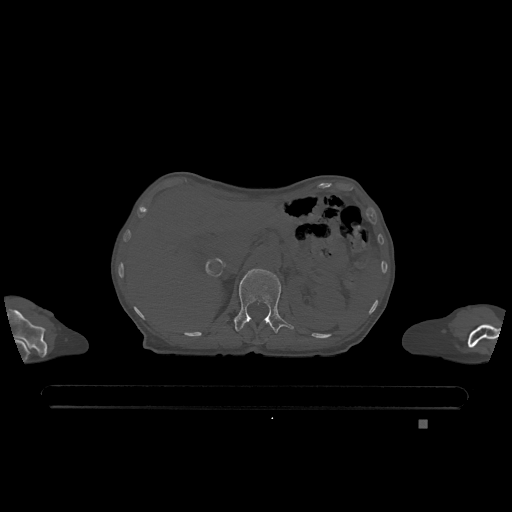
CT including the spine, one axial slice. Position 484 of 1317 along the scan axis. Bone window (W 1800 / L 400 HU). 0.5 mm slice thickness. 512 × 512 image matrix. Patient: female, 74 years. Case-level facts recorded for this patient, not image findings: primary cancer: lung.
Annotated regions visible in this slice (semi-automatically segmented with operator editing):
- L1 vertebra: bounding box <234,269,294,333> (left, top, right, bottom; pixels)
- T12 vertebra: <258,341,260,344>